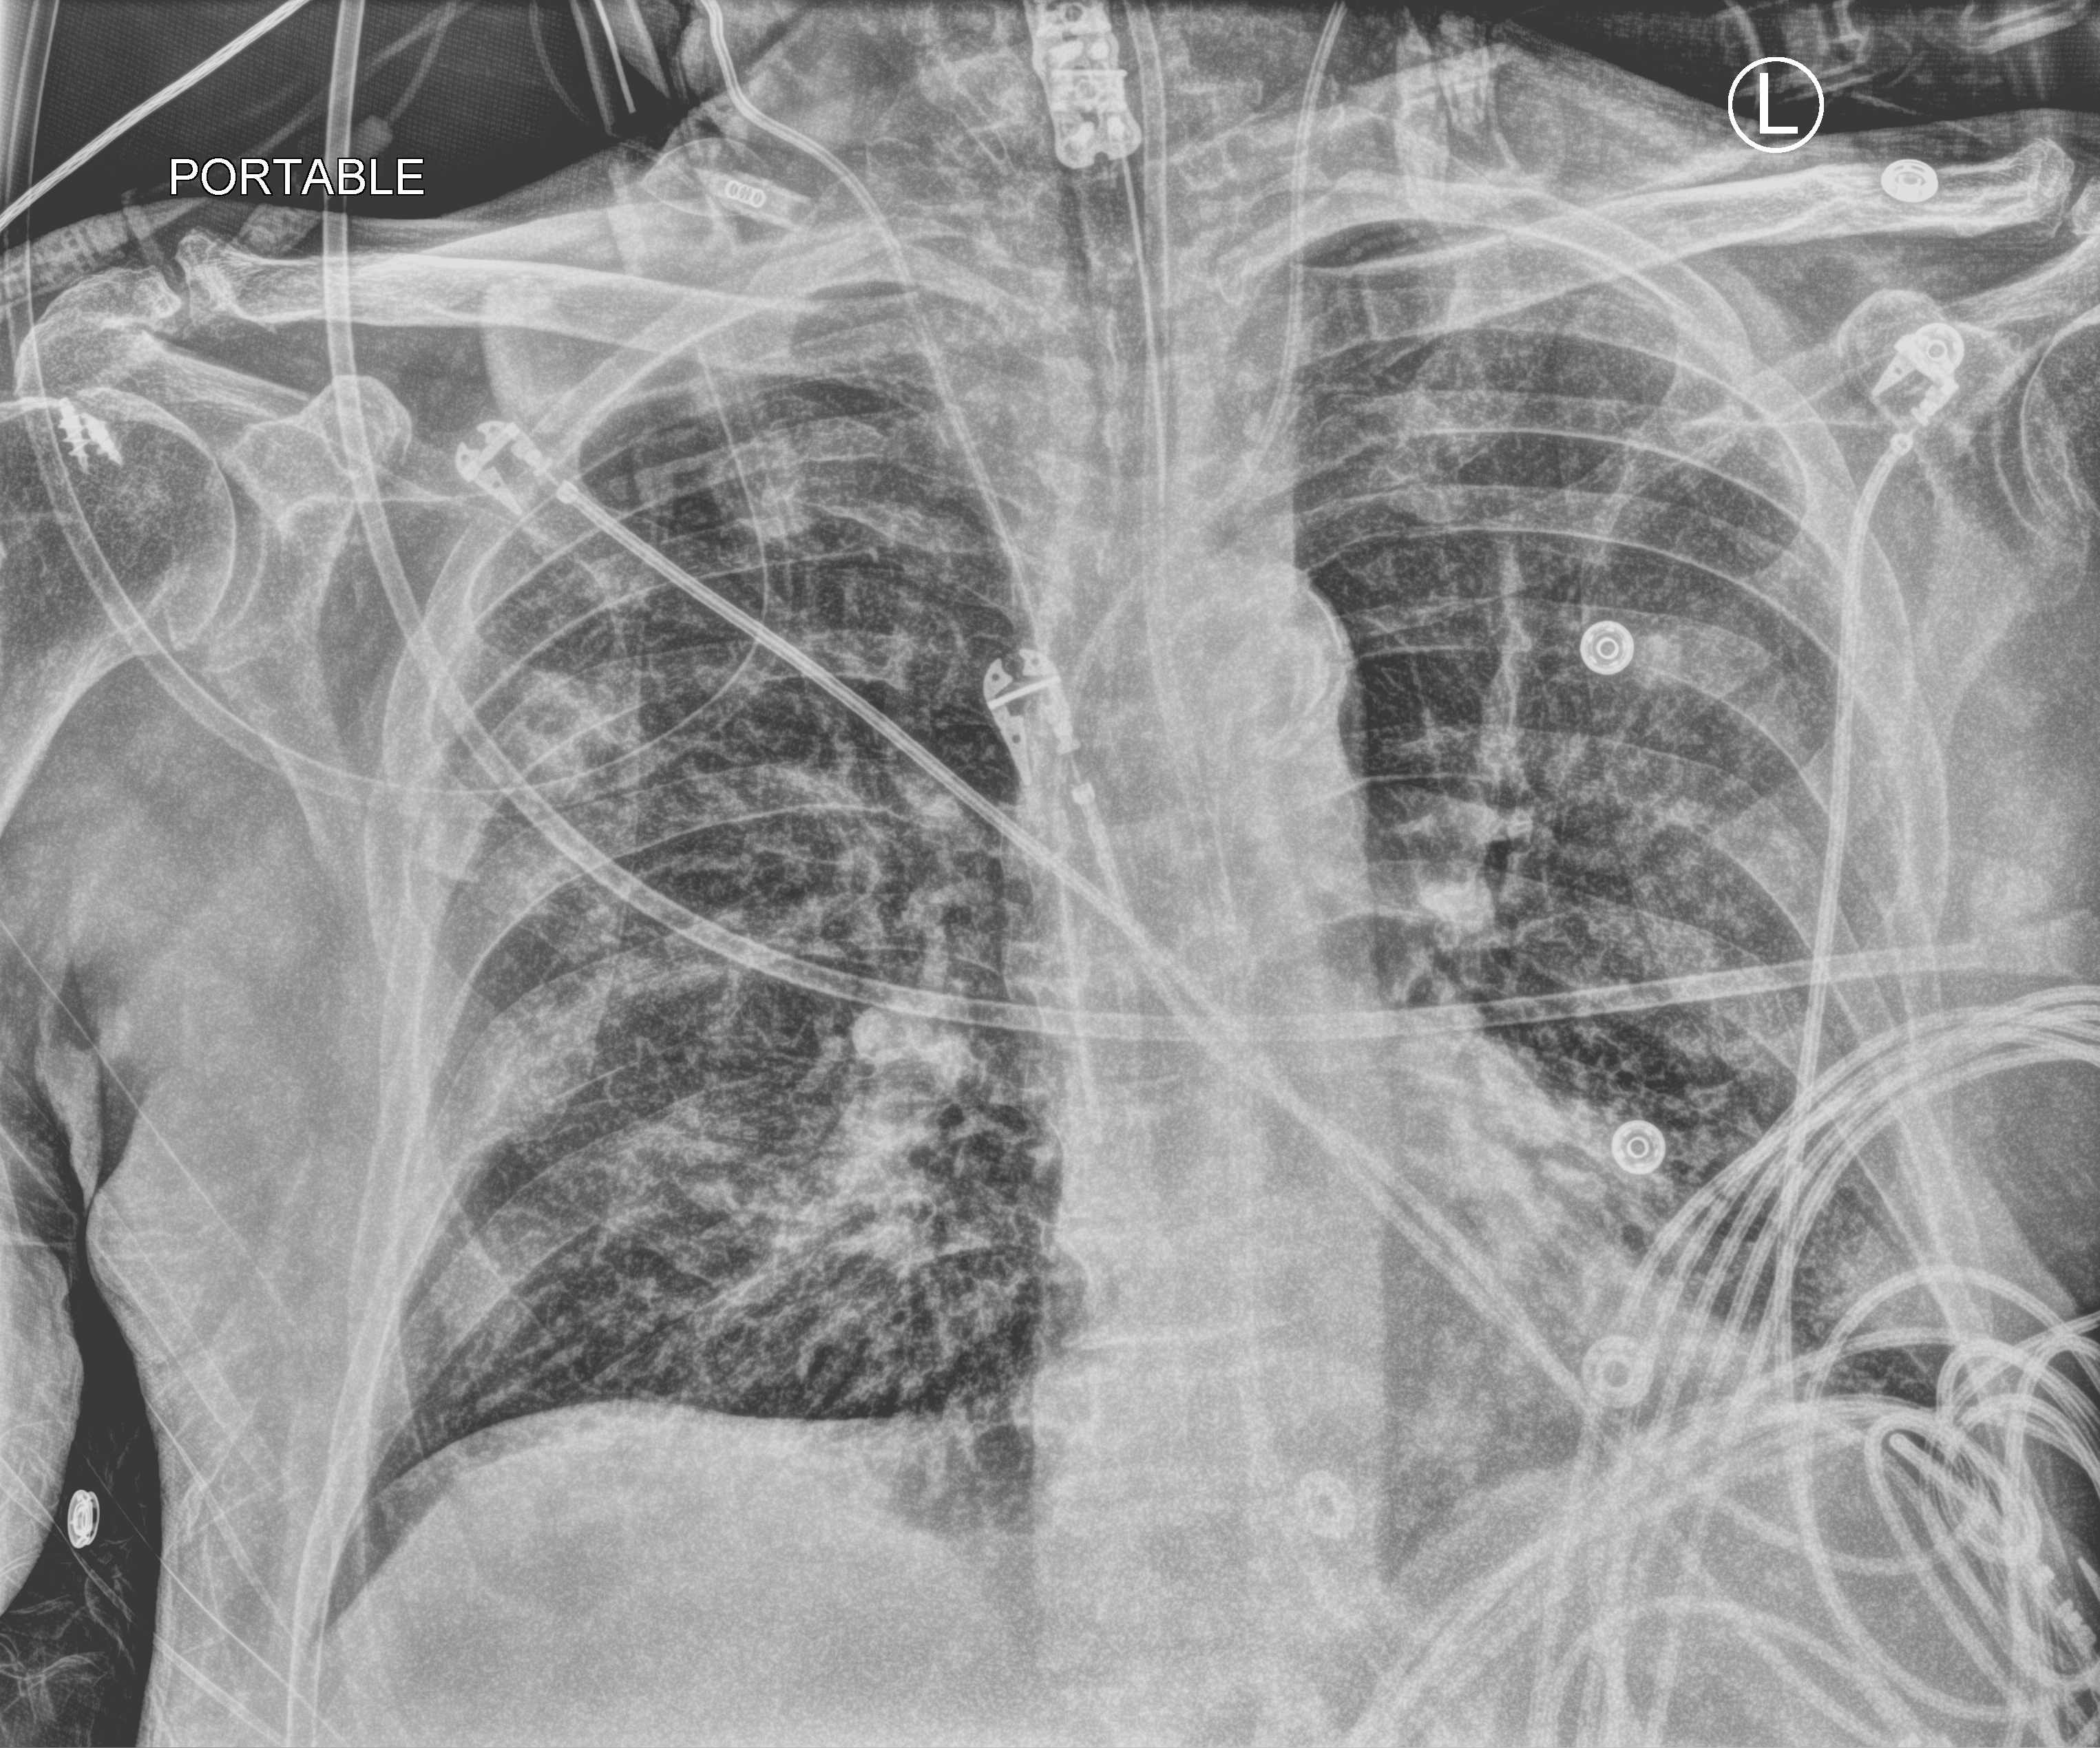
Portable chest radiograph; anteroposterior (AP) projection. Male patient hospitalised with COVID-19, age 75–90 years.
Hospital-stay facts (about this admission, not read from this image; timing relative to this image not recorded): diabetes (admission record): no; admitted to intensive care during this hospital stay: yes.